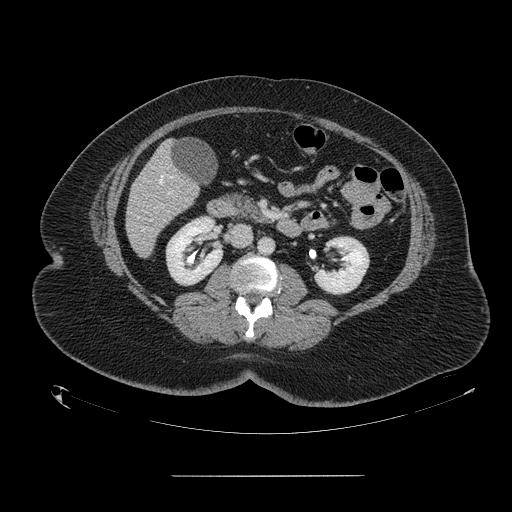
Contrast-enhanced abdominal CT, one axial slice; position 54 of 164 along the scan axis; 120 kVp; intravenous contrast given; soft-tissue window (W 400 / L 40 HU); 512 × 512 image matrix, field of view 495 × 495 mm. Female patient, age 52 years. Case-level facts recorded for this patient, not image findings: diagnosis: colorectal cancer liver metastases, imaged before liver resection; multiple liver metastases: yes; largest metastasis: 3.5 cm; chemotherapy before resection: no.
Structures marked on this image (manually delineated by an expert):
- hepatic veins: bounding box <137,175,174,218> (left, top, right, bottom; pixels)
- liver: <126,144,199,256>
- portal vein (with intrahepatic branches): <168,192,171,195>